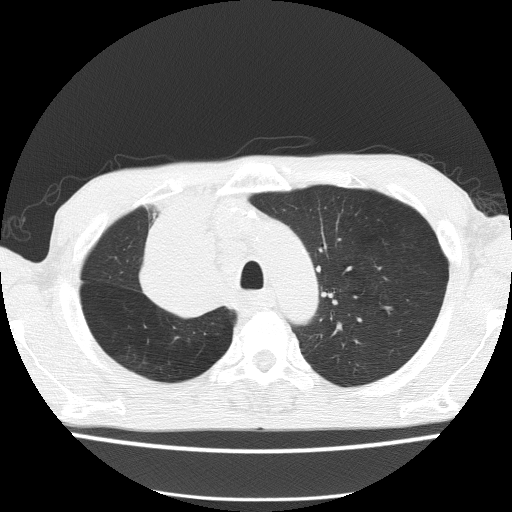
Low-dose screening chest CT, one axial slice. Slice 115 of 150 in the series (ordered by position). Reconstruction kernel FC51. 120 kVp. Lung window (W 1500 / L -600 HU). 2 mm slice thickness. 512 × 512 image matrix, field of view 336 × 336 mm.
Outlined on this slice (outlined manually by an expert reader):
- lesion 1 (tumor, hilum of right lung): bounding box [x1, y1, x2, y2] px = [142, 192, 219, 317]